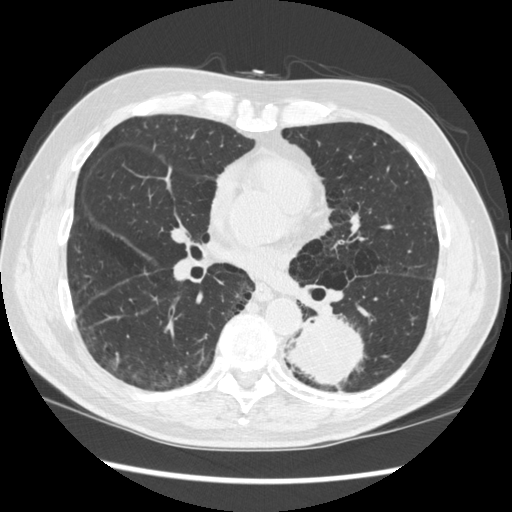
Low-dose screening chest CT, one axial slice. Slice 157 of 348 in the series (ordered by position). Lung window (W 1500 / L -600 HU). 512 × 512 image matrix, field of view 360 × 360 mm.
Outlined on this slice (manually delineated by an expert):
- lesion 1 (tumor, lower lobe of left lung): bounding box [x1, y1, x2, y2] px = [288, 316, 364, 386]